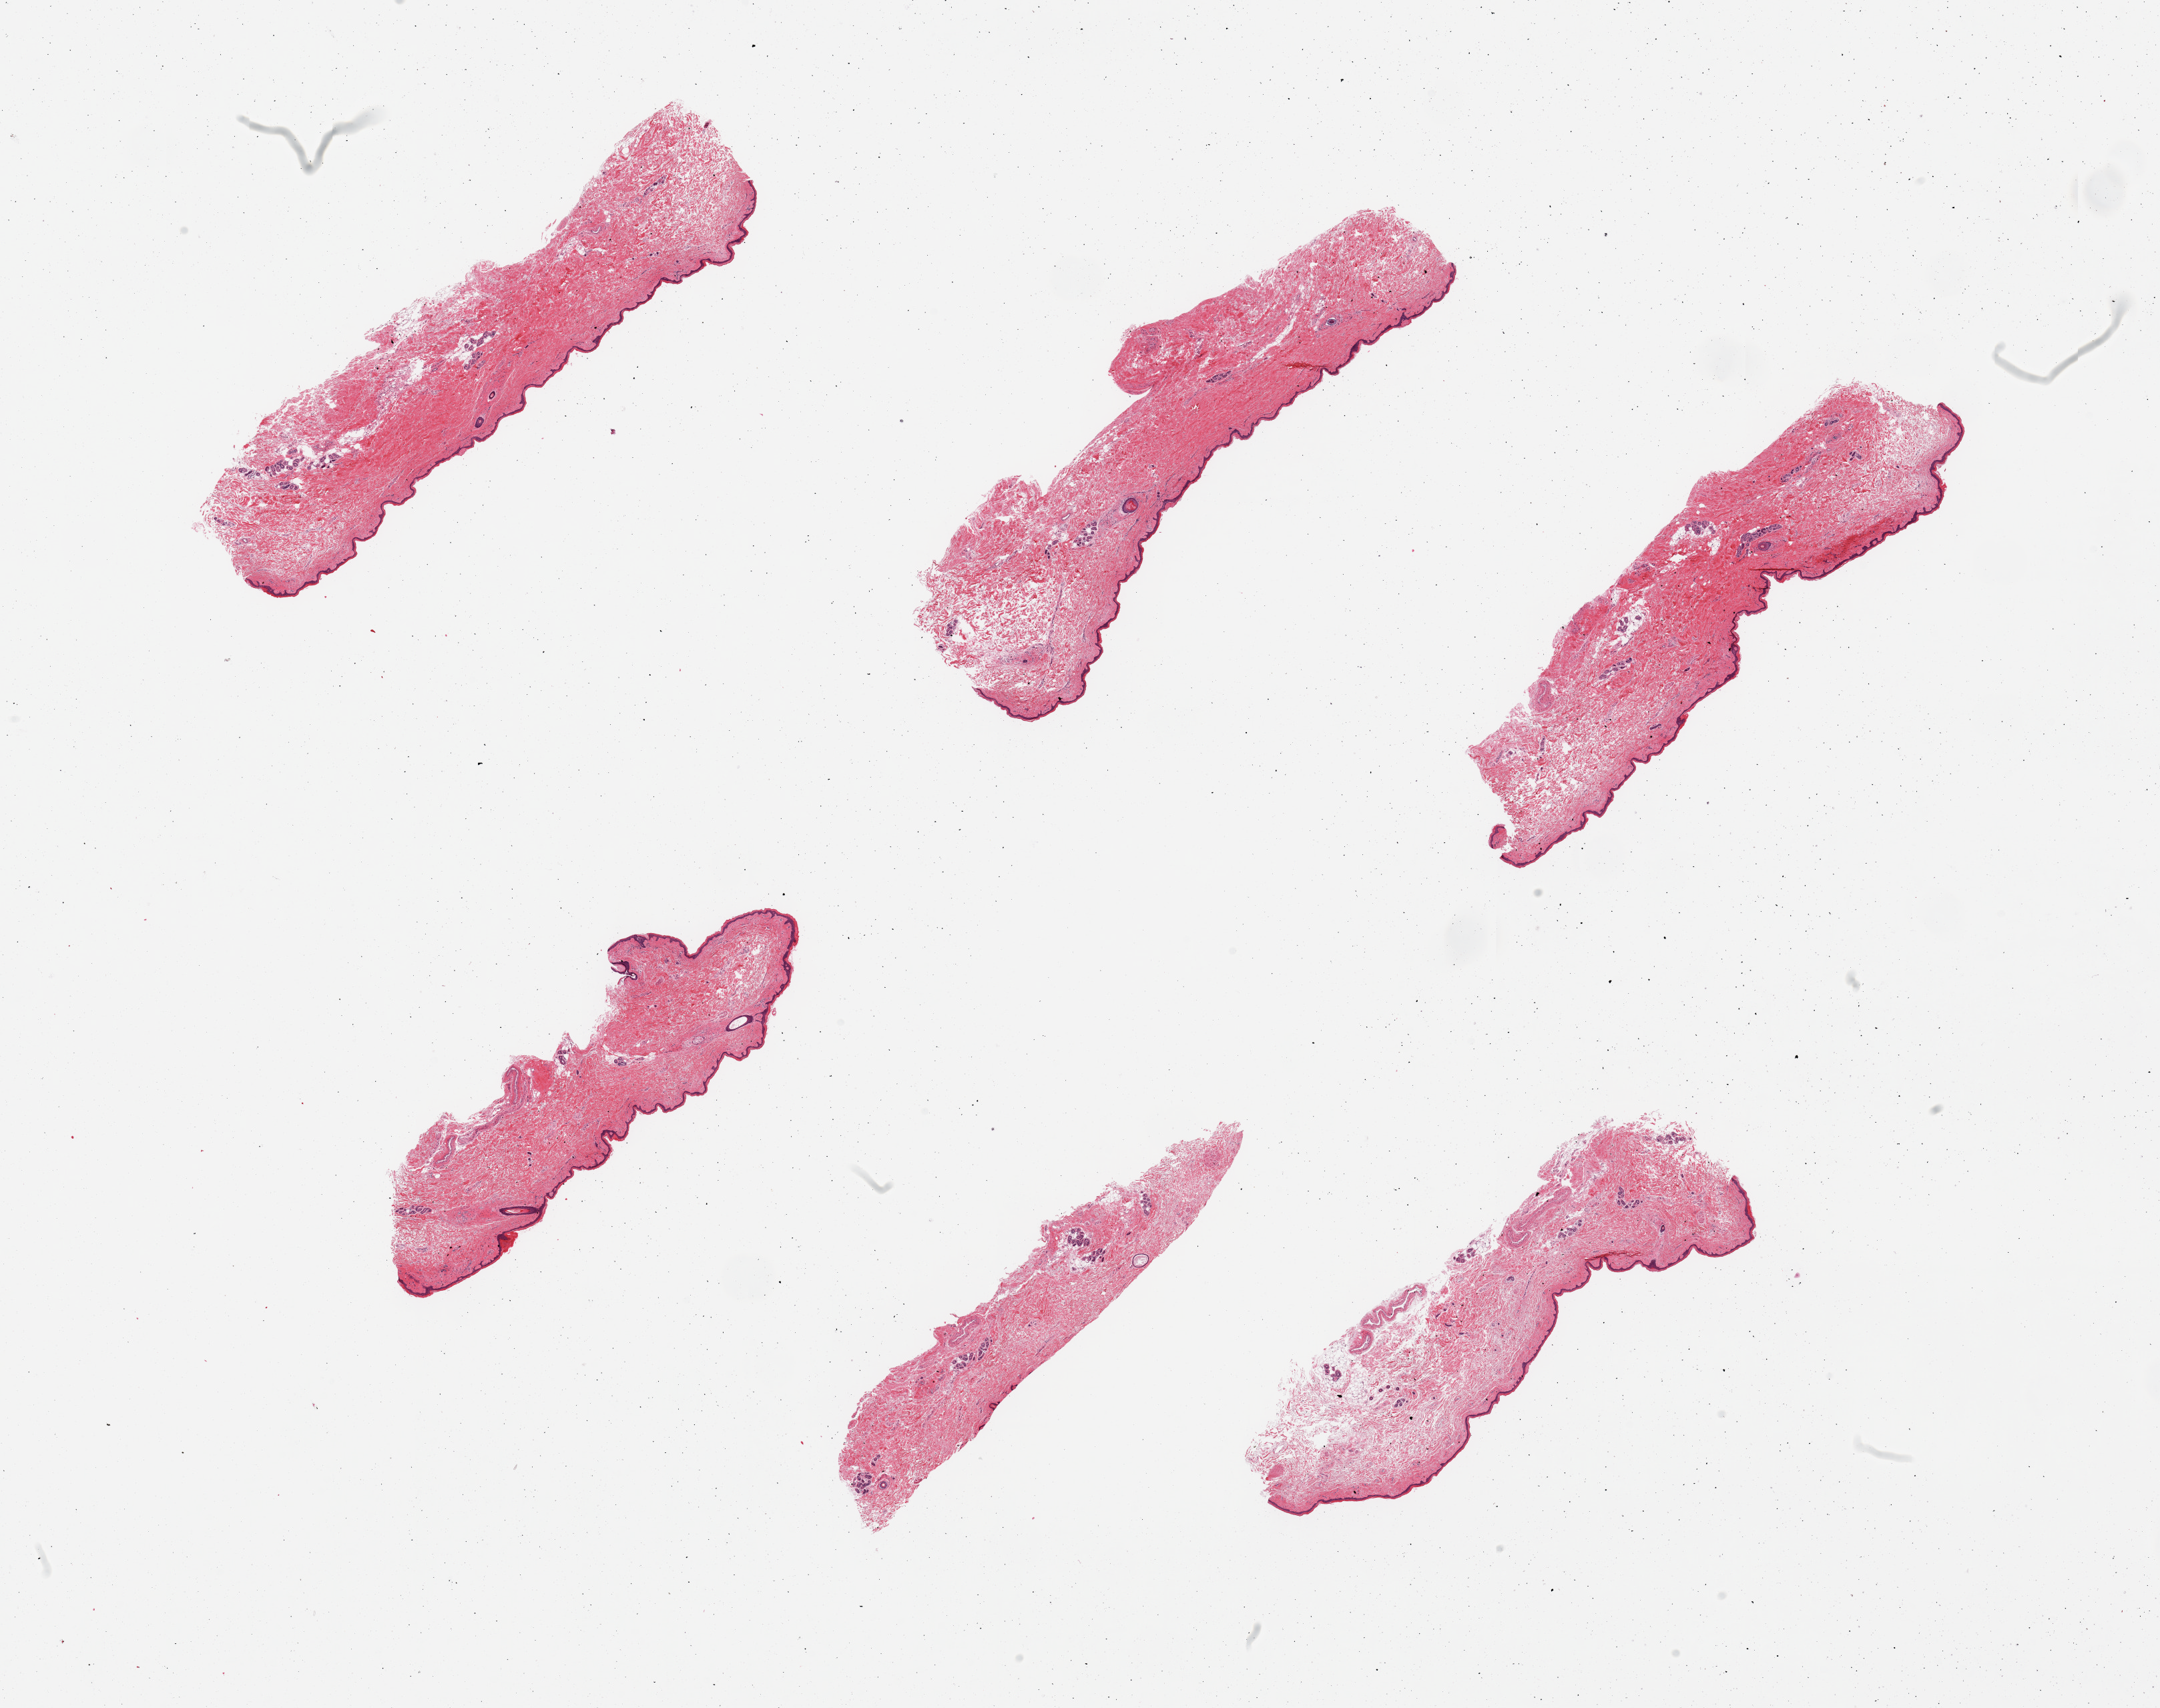
Digitized hematoxylin and eosin (H&E)-stained section, low-resolution overview of the scanned area, about 25.6 x 20.2 mm. PAXgene-fixed, paraffin-embedded tissue. Target tissue: skin of suprapubic region. Tissue donor sample. Donor sex: female.
* reviewer comment on this tissue sample: 6 pieces; well trimmed; minimal dermal fat